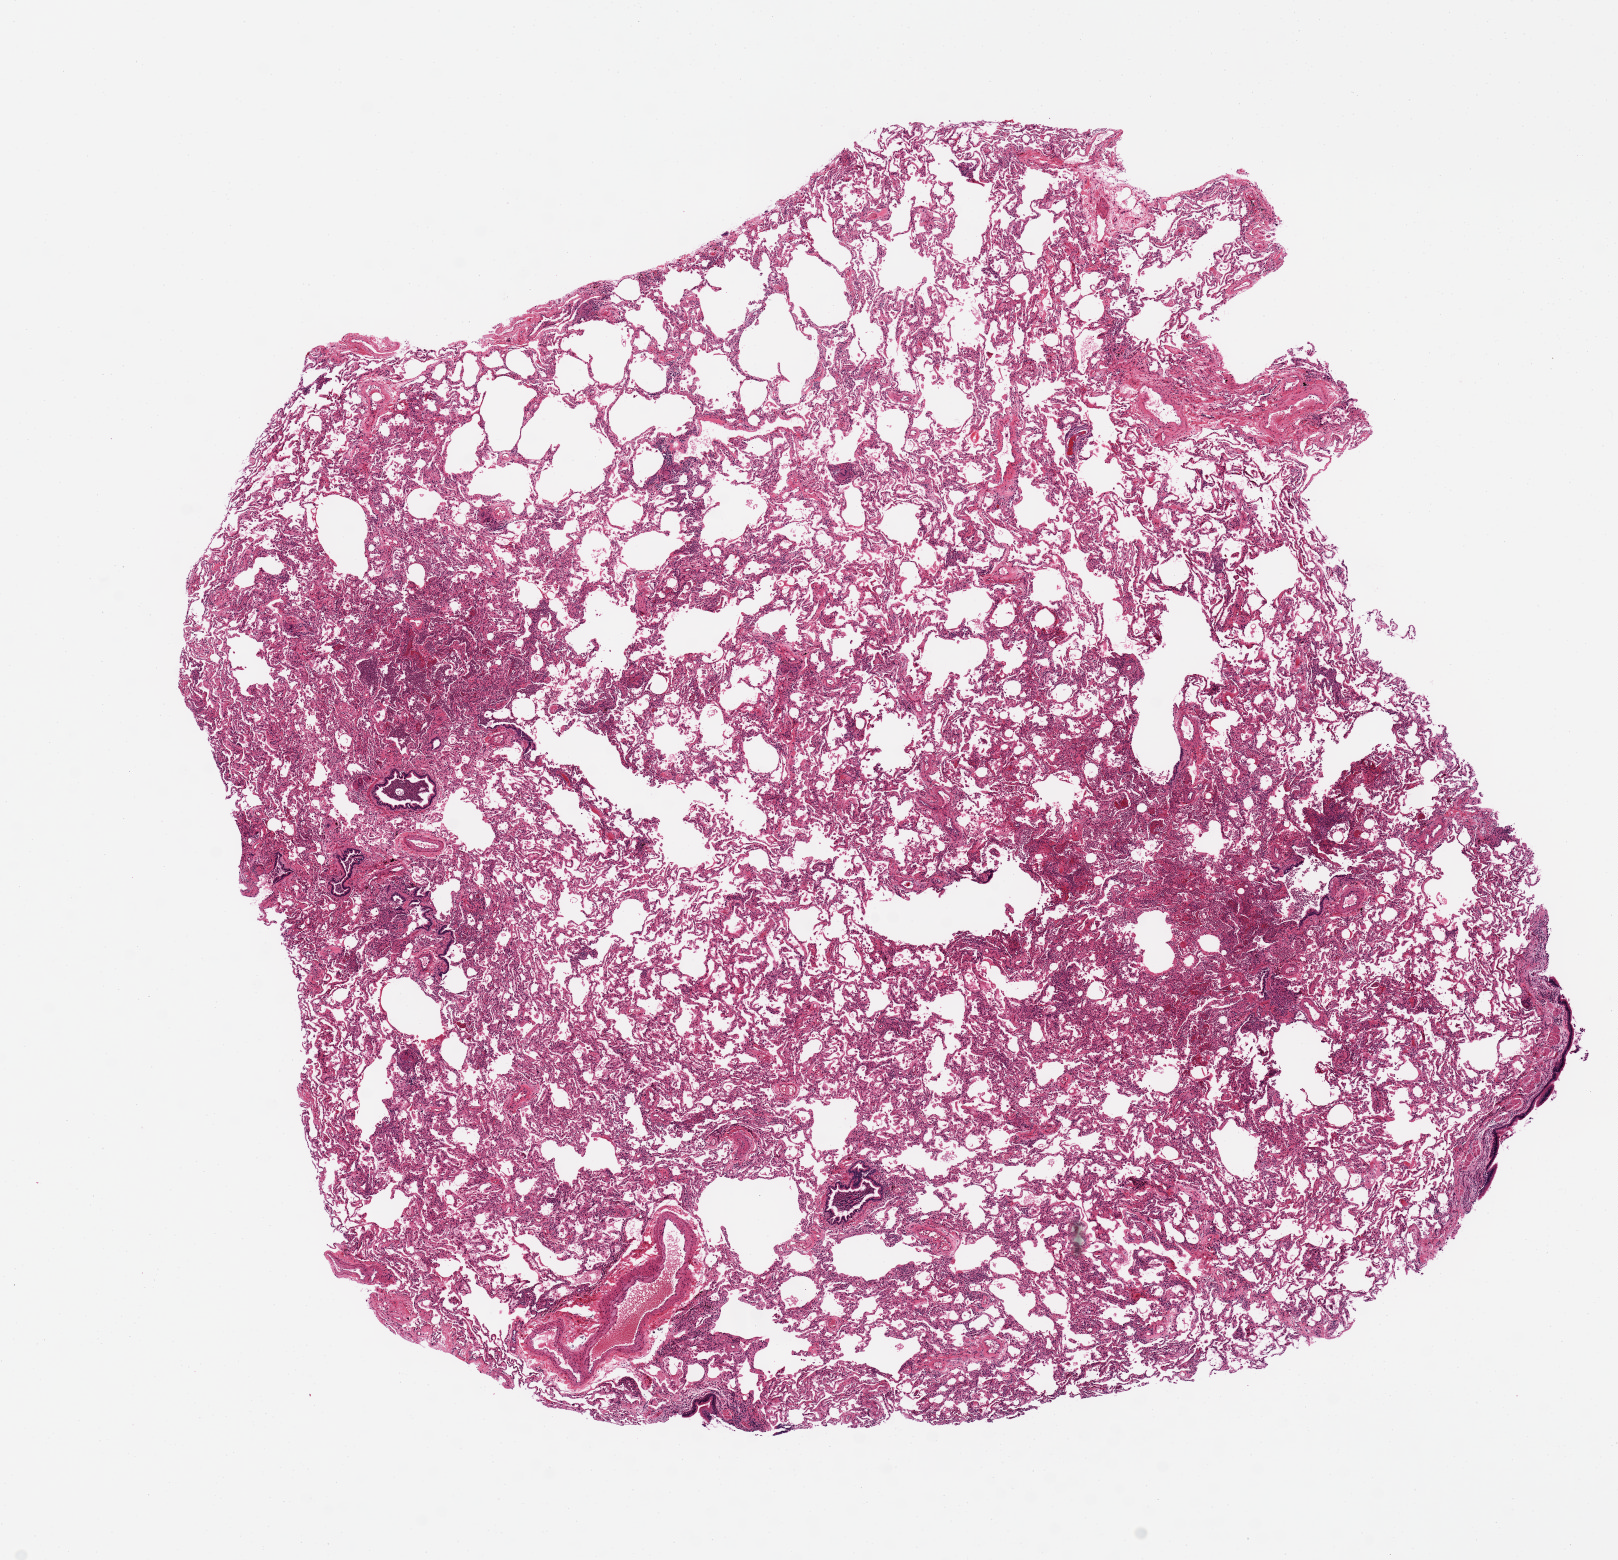
Hematoxylin and eosin (H&E) whole-slide image, a low-resolution overview of the entire scanned area, about 12.8 x 12.3 mm, PAXgene-fixed, paraffin-embedded tissue, sampled site (target tissue): lung, donor tissue sample.
Review note (as recorded): Bronchopneumonia; aspiration?.